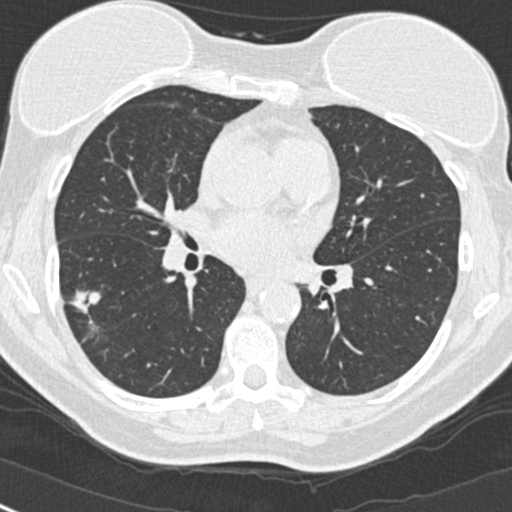
Low-dose screening chest CT, one axial slice; slice 137 of 268 in the series (ordered by position); 120 kVp; lung window (W 1500 / L -600 HU); 512 × 512 image matrix, field of view 296 × 296 mm.
Structures marked on this image (outlined manually by an expert reader):
- lesion 1 (tumor, upper lobe of right lung): bounding box (x1, y1, x2, y2) in pixels: (69, 290, 100, 313)